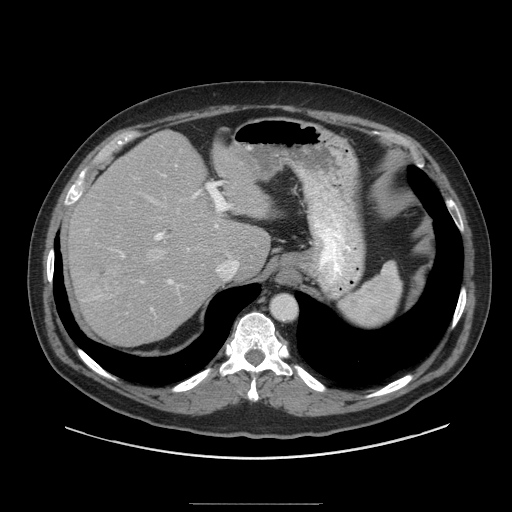
Contrast-enhanced abdominal CT (liver protocol), one axial slice. Position 70 of 91 along the scan axis. Reconstruction kernel STANDARD. 140 kVp. Soft-tissue window (W 400 / L 40 HU). 2.5 mm slice thickness. 512 × 512 image matrix, field of view 440 × 440 mm. Case-level facts recorded for this patient, not image findings: diagnosis: hepatocellular carcinoma (patient treated with transarterial chemoembolisation; whether this scan precedes or follows treatment is not stated here); TNM stage (as recorded): Stage-I; Child-Pugh class: A; tumour nodularity: uninodular.
Outlined on this slice (semi-automatic segmentation, software-assisted and operator-edited):
- abdominal aorta: bounding box <272,296,296,320> (left, top, right, bottom; pixels)
- liver parenchyma outside the tumour (the mass and vessels are separate outlines, so this box may not span the whole liver): <68,130,270,344>
- mass: <90,257,128,295>
- liver vessels: <87,174,239,311>